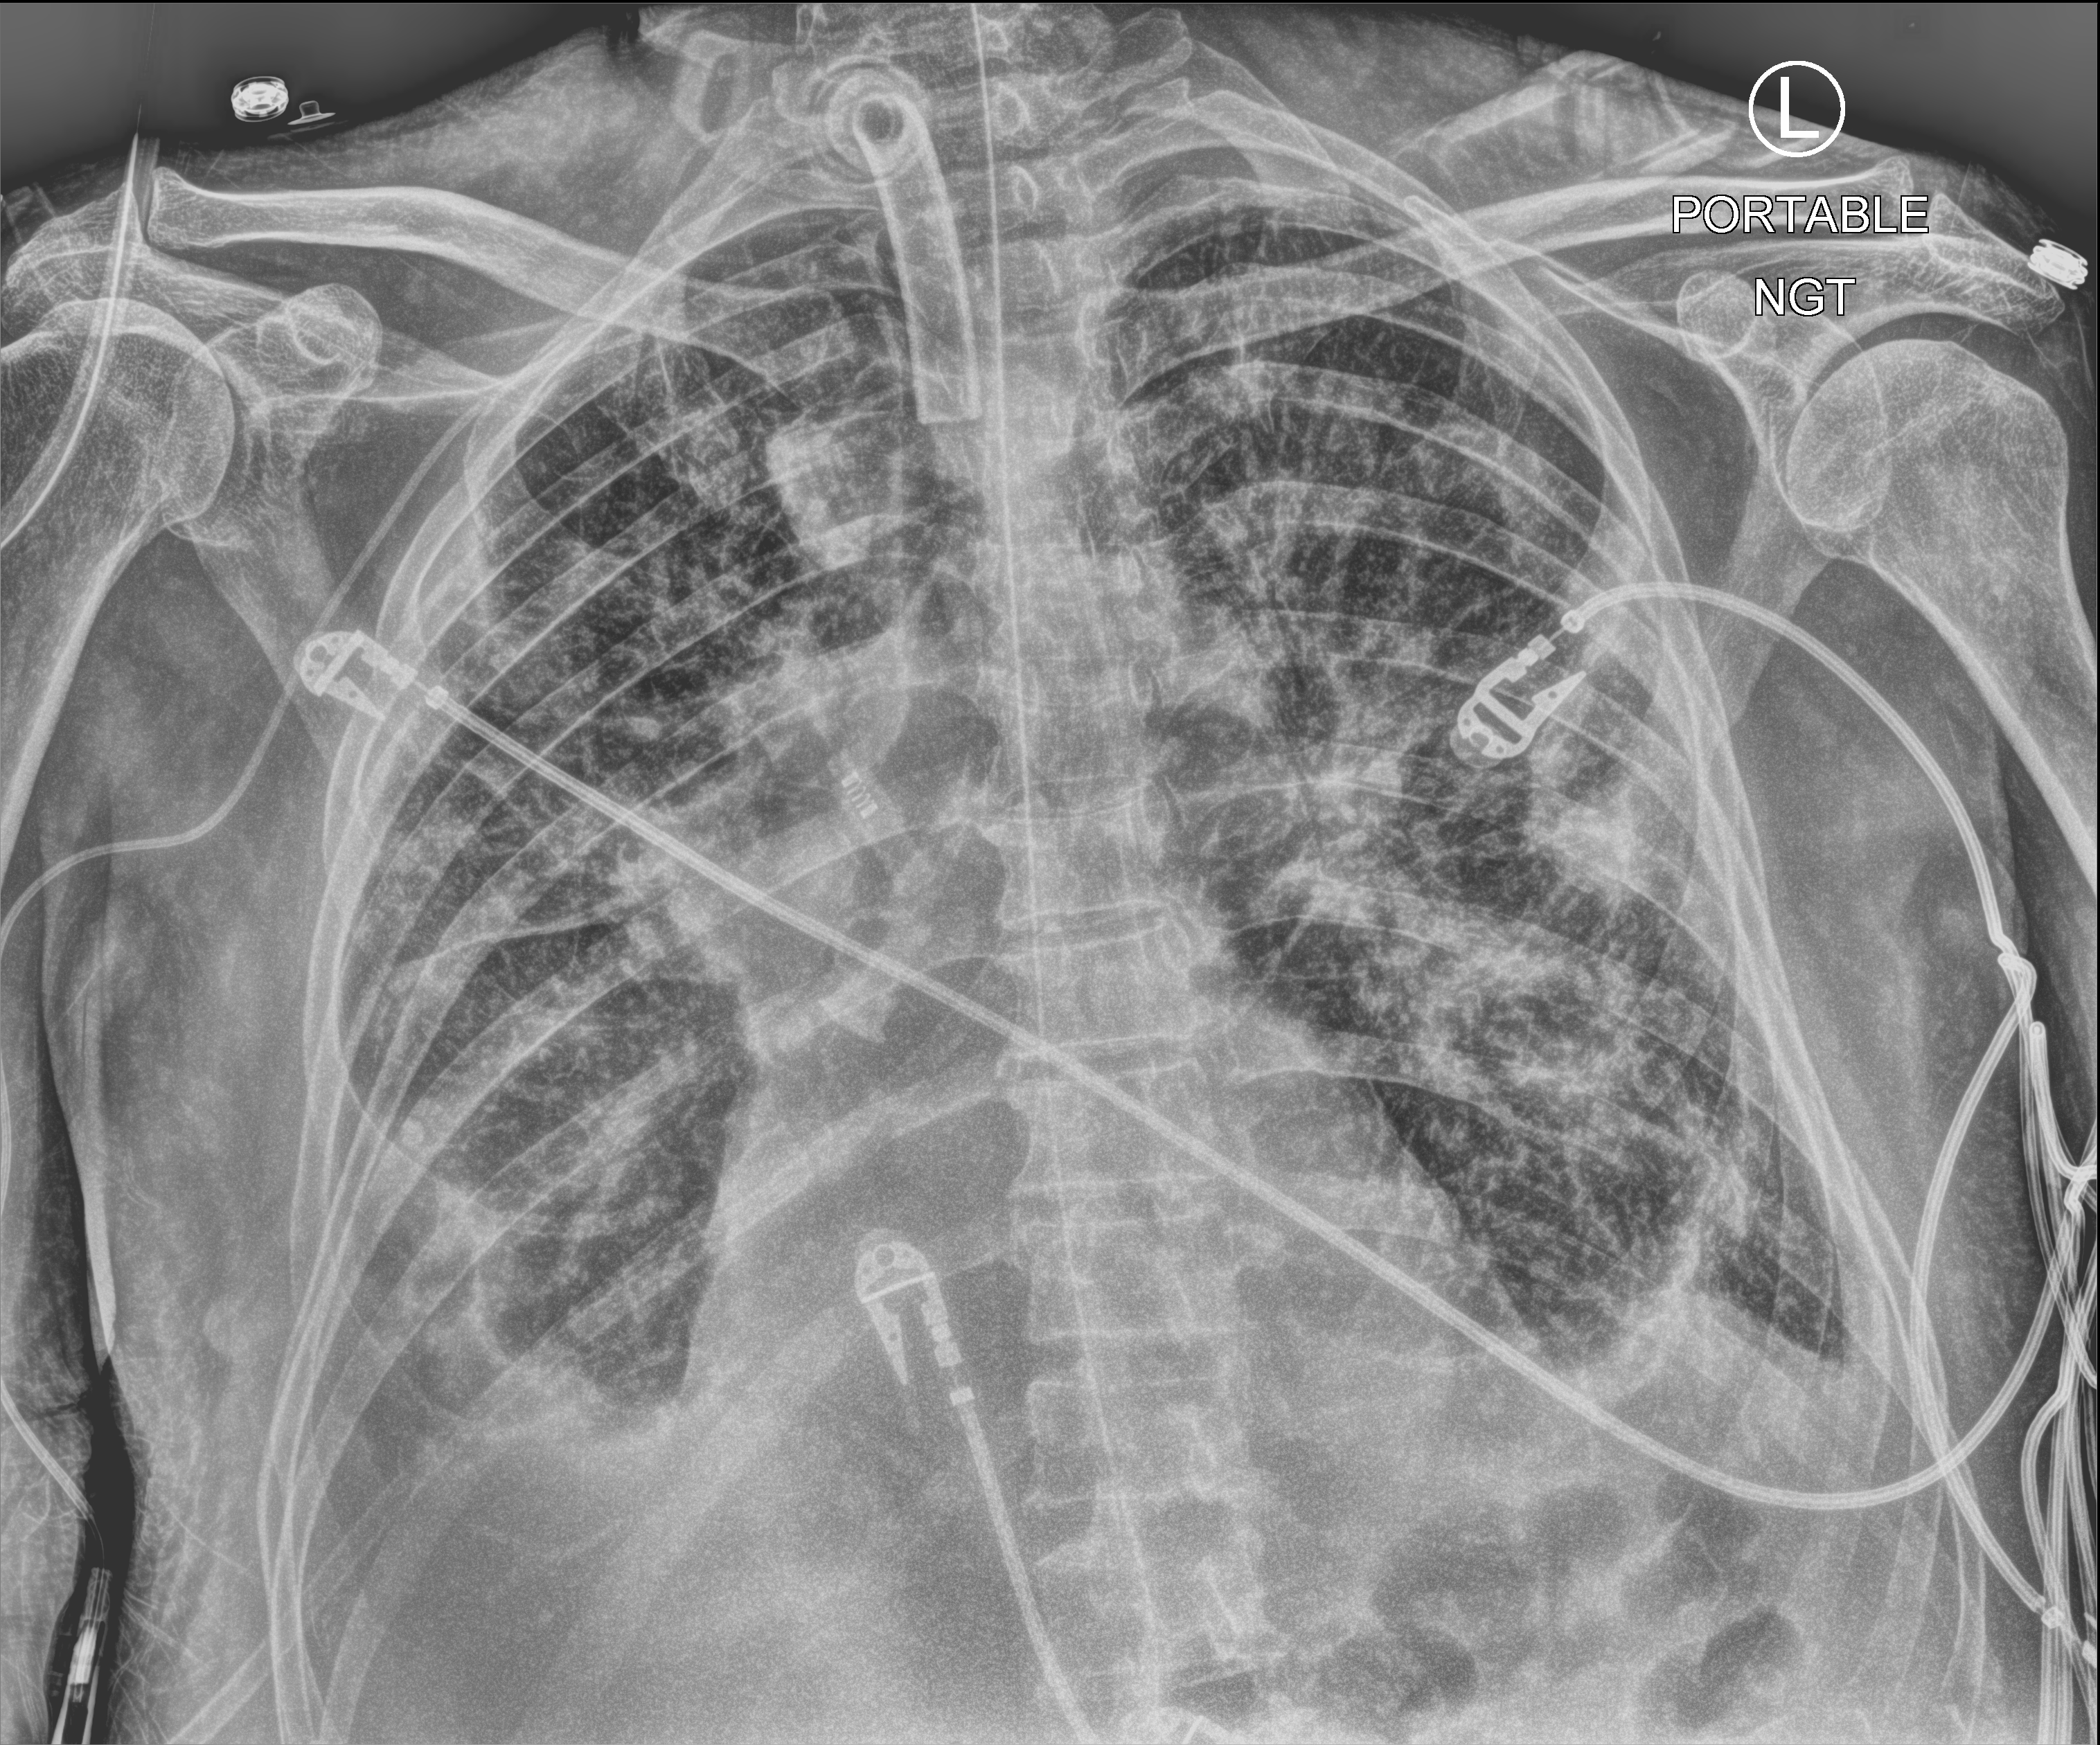
Chest X-ray (portable). Male patient hospitalised with COVID-19, age 75–90 years.
From the hospital-stay record, not from the radiograph (when in the stay this image was taken is not recorded):
- admitted to intensive care during this hospital stay: yes